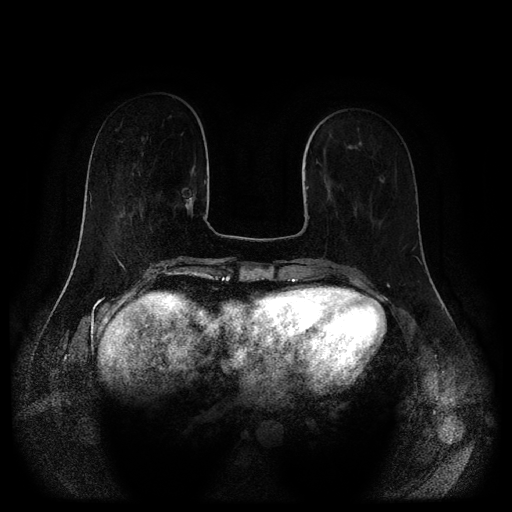
Breast MRI (dynamic contrast-enhanced, multi-phase), one axial slice. Slice 37 of 116 in the series (ordered by position). Dynamic contrast-enhanced series, time point 2 of 5 at this slice position (early post-contrast). 1.5 T. TE 2.6 ms, TR 5.2 ms. 2 mm slice thickness. 512 × 512 image matrix. Patient: female, 62 years.
Outlined on this slice (semi-automatically segmented with operator editing):
- breast lesion (labelled 'tumour' in the annotation; benign lesions carry a separate 'benign' label): bounding box (x1, y1, x2, y2) in pixels: (178, 190, 195, 212)